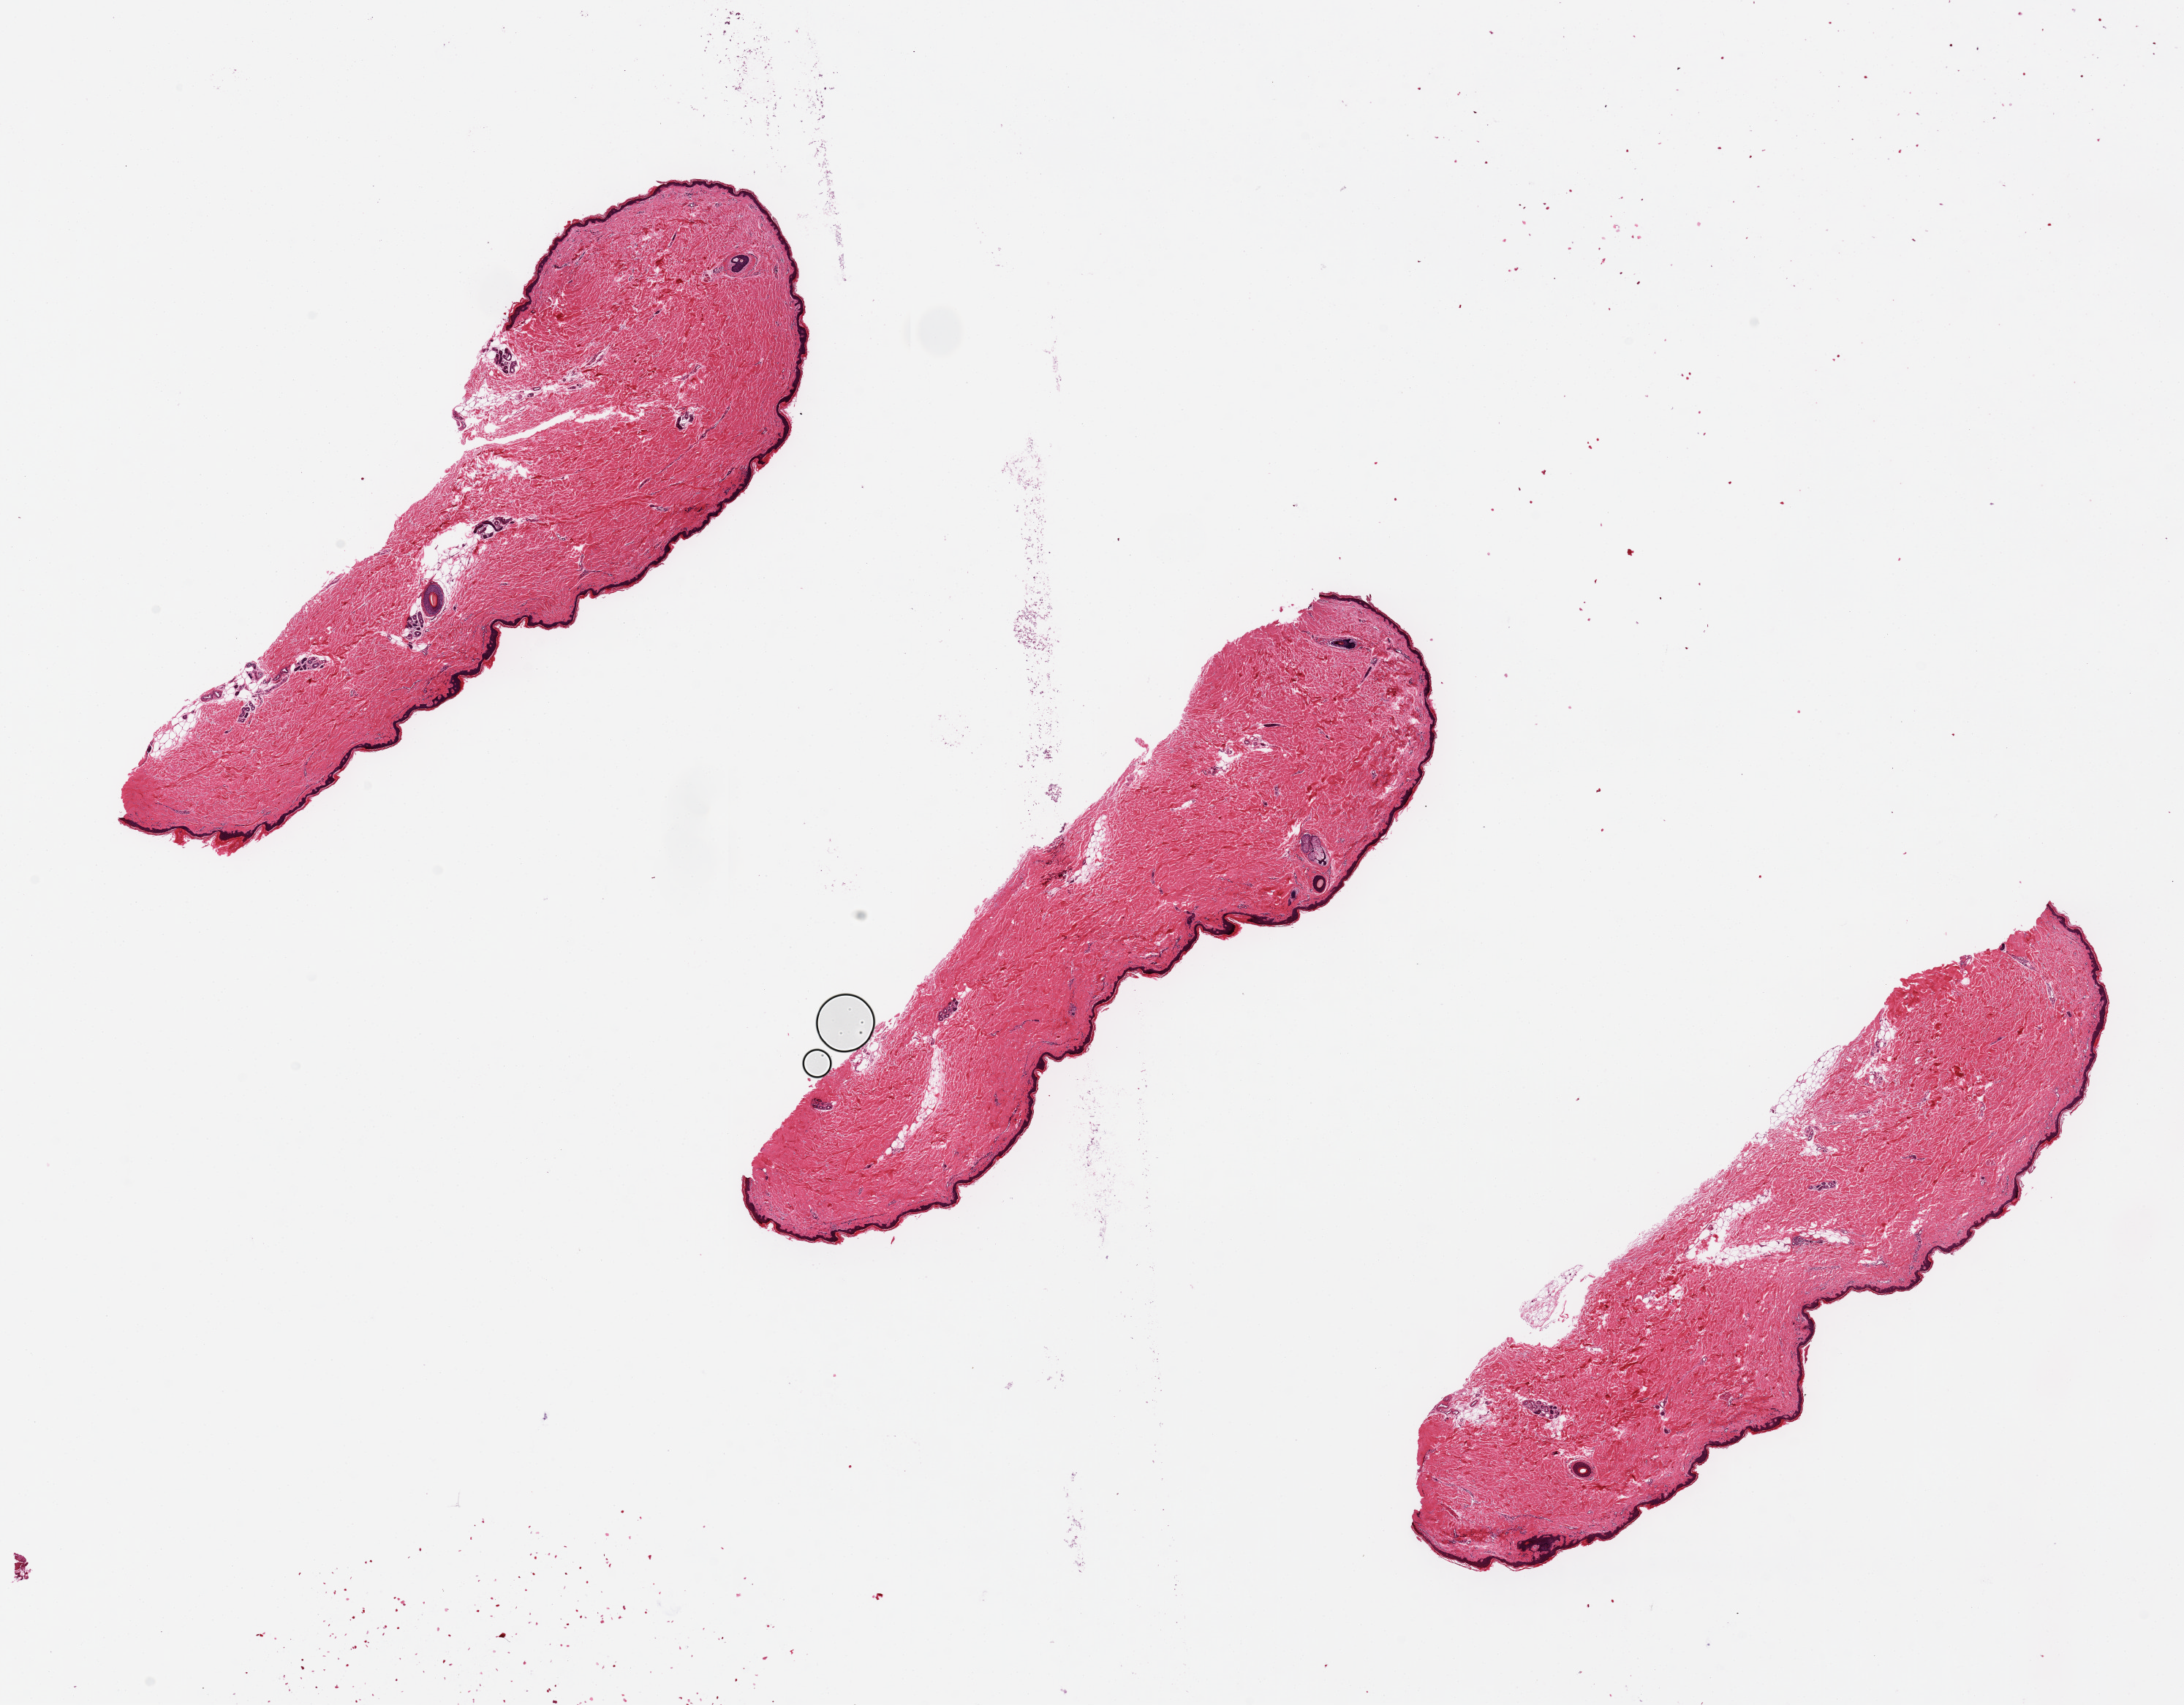
Hematoxylin and eosin (H&E) whole-slide image, brightfield, shown as a low-resolution overview of the whole scanned area (about 23.6 x 18.4 mm). PAXgene-fixed, paraffin-embedded tissue. Sampled site (target tissue): skin of lower leg. Donor tissue sample. Donor sex: male.
Pathologist's review note for this sample: Epidermis is 3% of aliquot thickness.